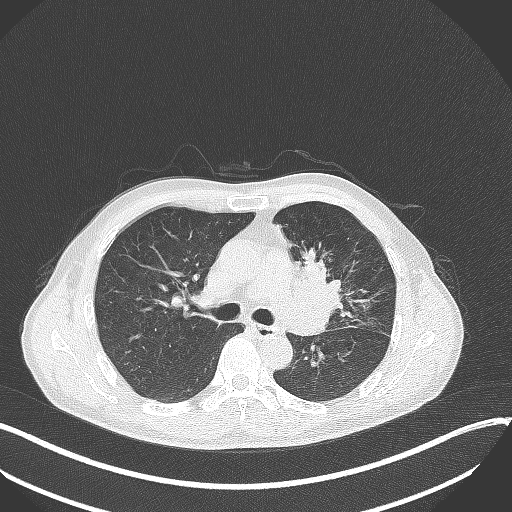
Chest CT, one axial slice. Position 210 of 411 along the scan axis. 120 kVp. Lung window (W 1500 / L -600 HU). 1 mm slice thickness. 512 × 512 image matrix, field of view 400 × 400 mm. Patient: male, 56 years. From the clinical record (not read from this slice): clinical TNM (as recorded): T2a N0 M0.
Annotated regions visible in this slice (rectangle marked by the reading radiologist):
- lung tumour (recorded histology: squamous cell carcinoma): box from (x=284, y=245) to (x=347, y=324) px